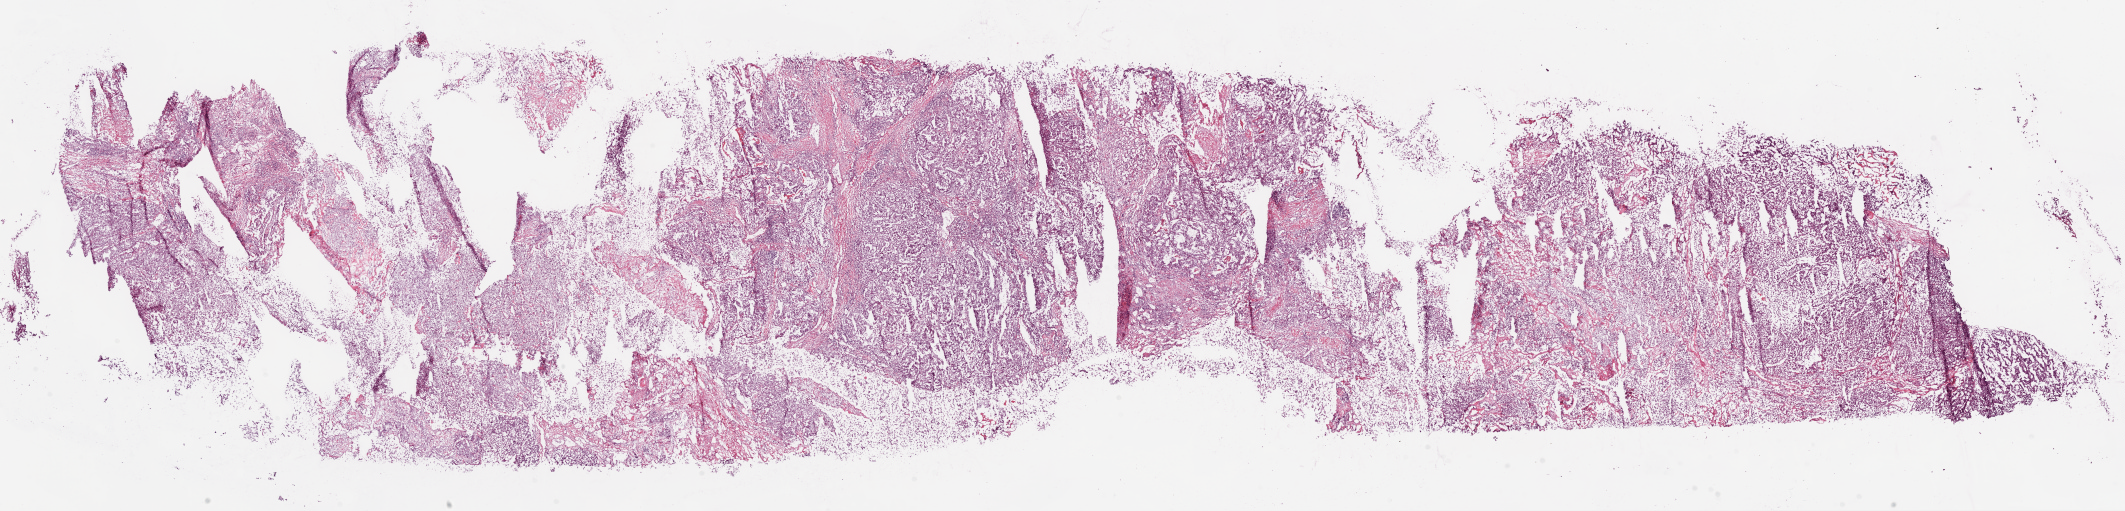
H&E-stained whole-slide image, low-resolution overview of the scanned area, about 34.1 x 8.2 mm (from a 20x scan). Frozen section. Primary tumour sample from the kidney. Patient: male, age at initial diagnosis 57 years. Histologic grade: G3 (poorly differentiated). Slide review estimates, as recorded: tumour cells 80%, tumour nuclei 80%, normal cells 0%, stromal cells 20%, necrosis 0%.
AJCC pathologic stage: III. Pathologic diagnosis: Clear cell adenocarcinoma, NOS. TNM: T3a NX M0.